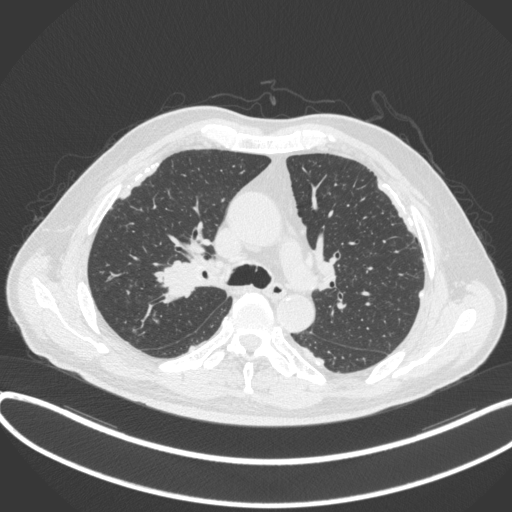
Chest CT, one axial slice. Slice 280 of 455 in the series (ordered by position). Lung window (W 1500 / L -600 HU). 1 mm slice thickness. 512 × 512 image matrix. Patient: male, 58 years. Case-level facts recorded for this patient, not image findings: clinical TNM (as recorded): T1c N0 M0.
Outlined on this slice (bounding box drawn by a radiologist):
- lung tumour (recorded histology: squamous cell carcinoma): bounding box <151,255,204,307> (left, top, right, bottom; pixels)